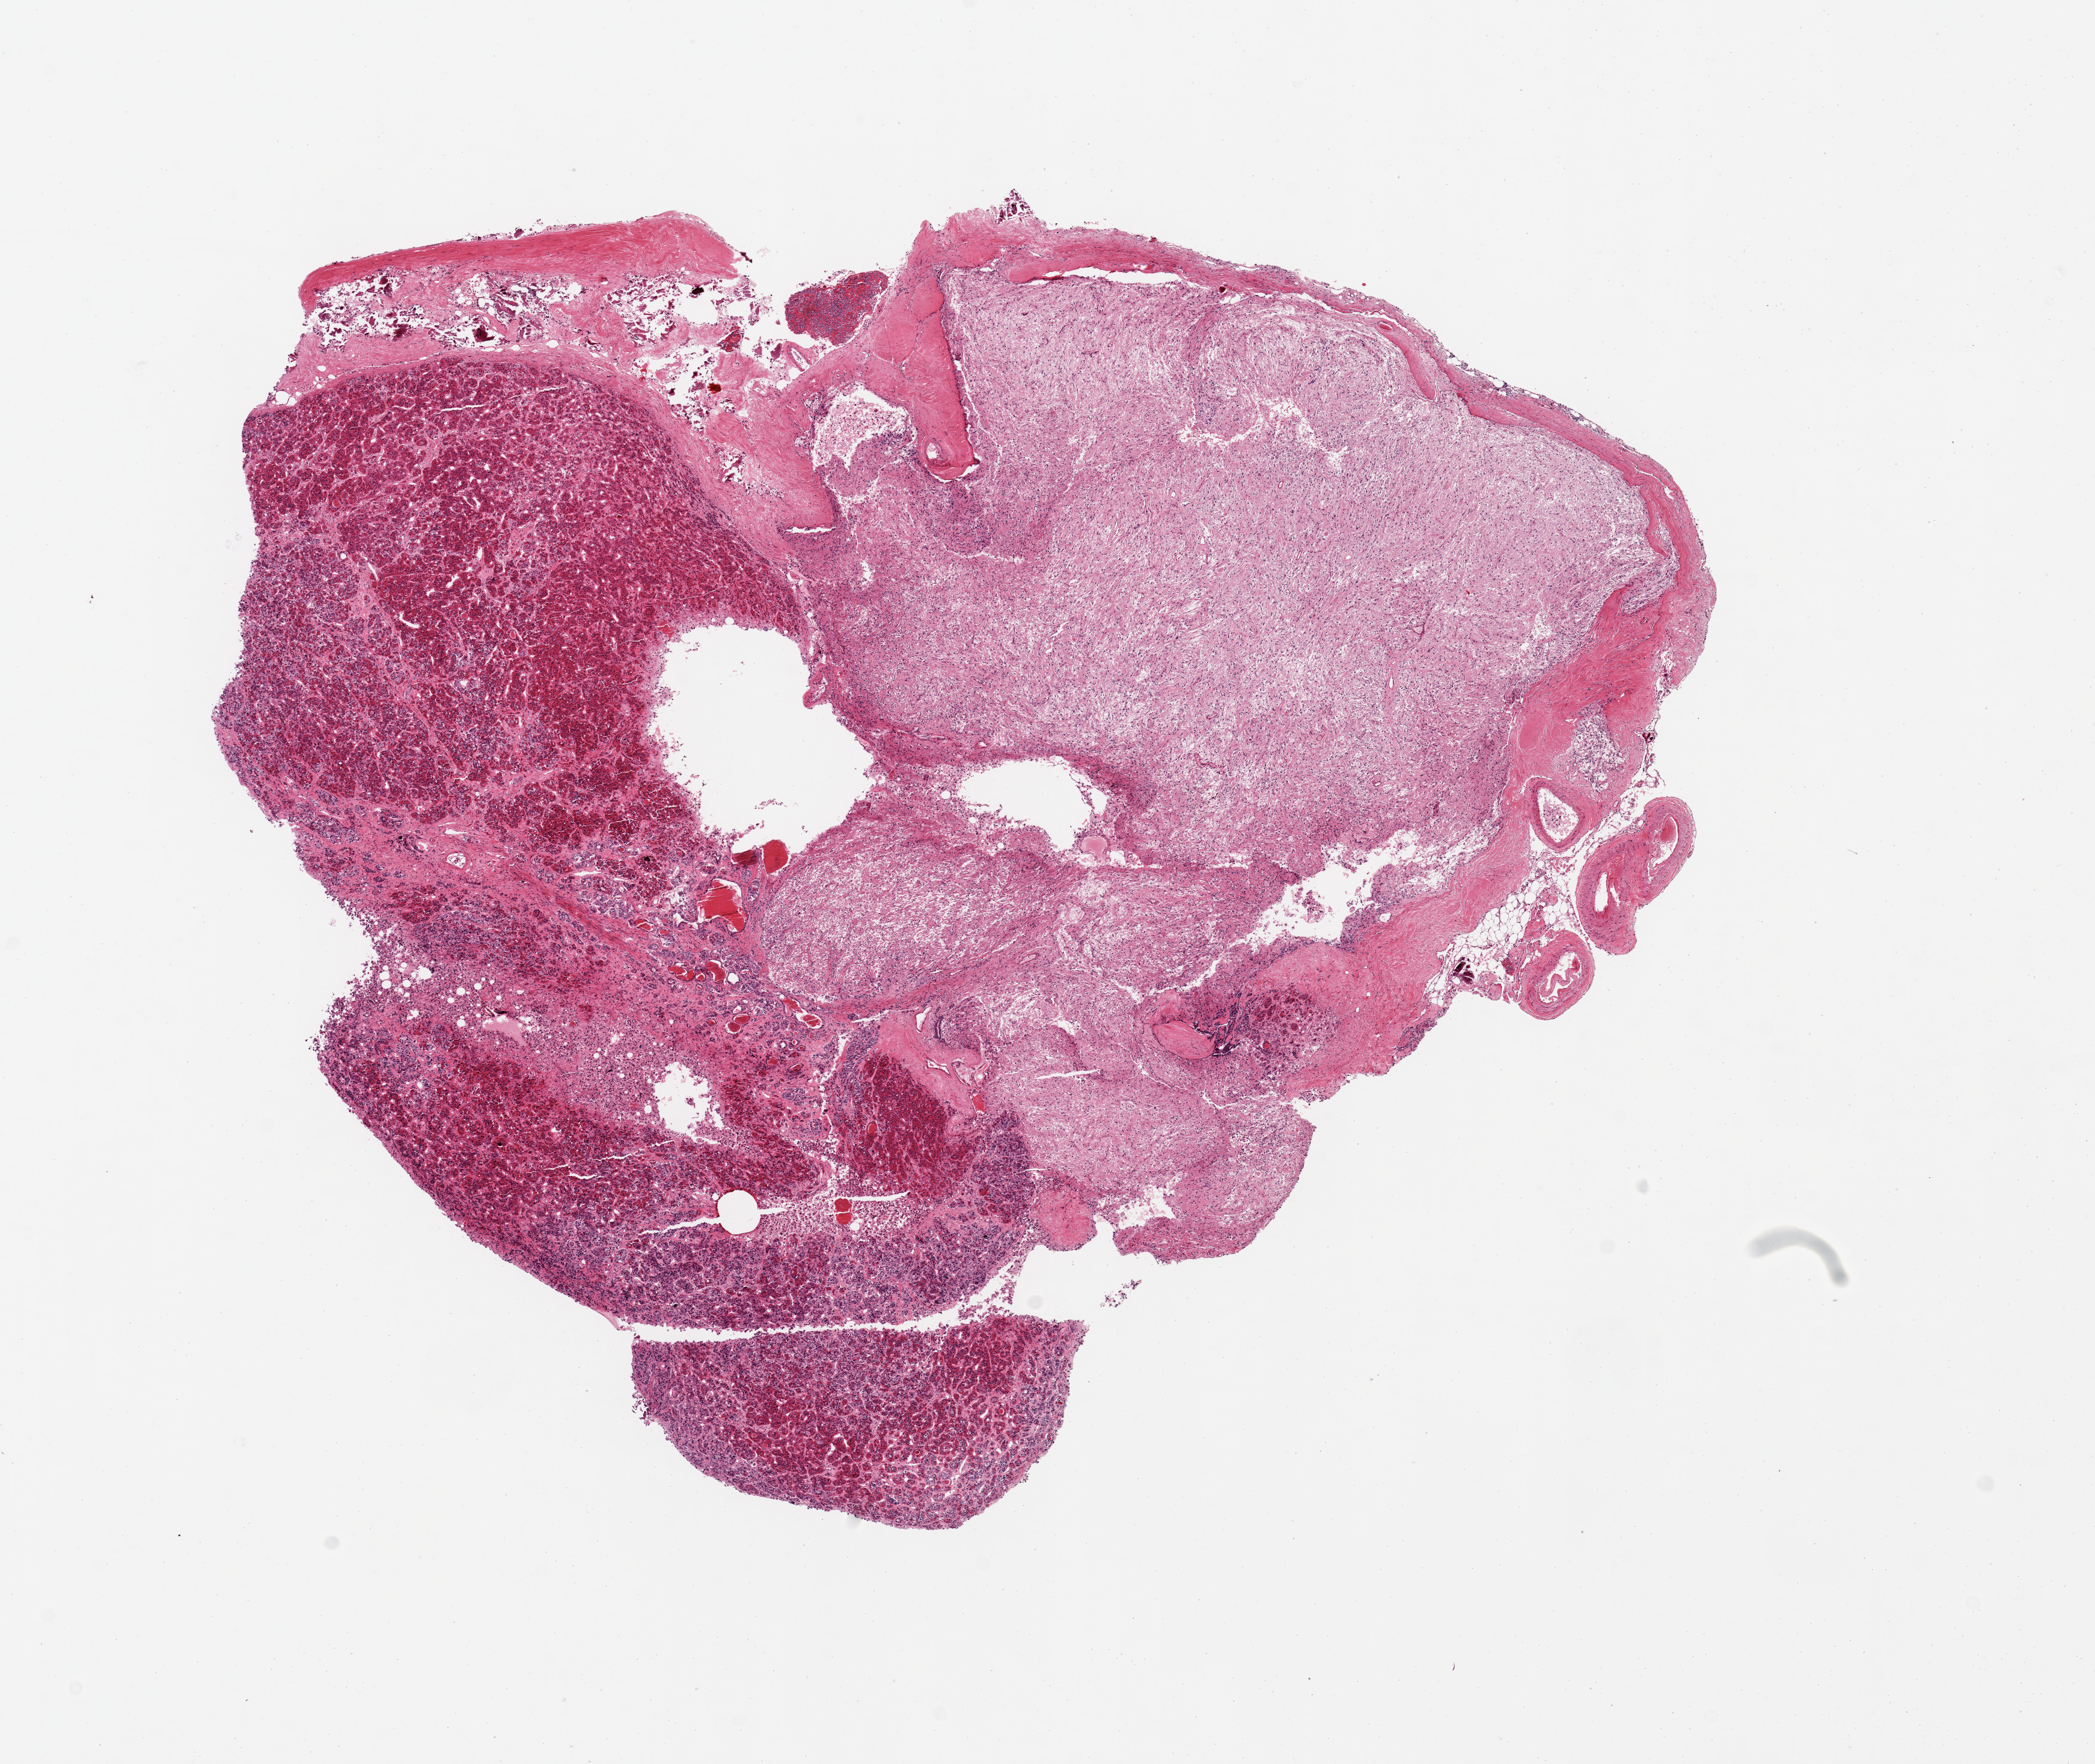
Whole-slide image, haematoxylin and eosin stain, low-resolution overview of the scanned area, about 13.8 x 11.6 mm (from a 20x scan), PAXgene-fixed paraffin-embedded (PFPE) section, target tissue: pituitary, donor tissue sample. Donor sex: male.
Reviewer comment on this tissue sample: 1 piece, ~50% each adenohypophysis & neurohypophysis.